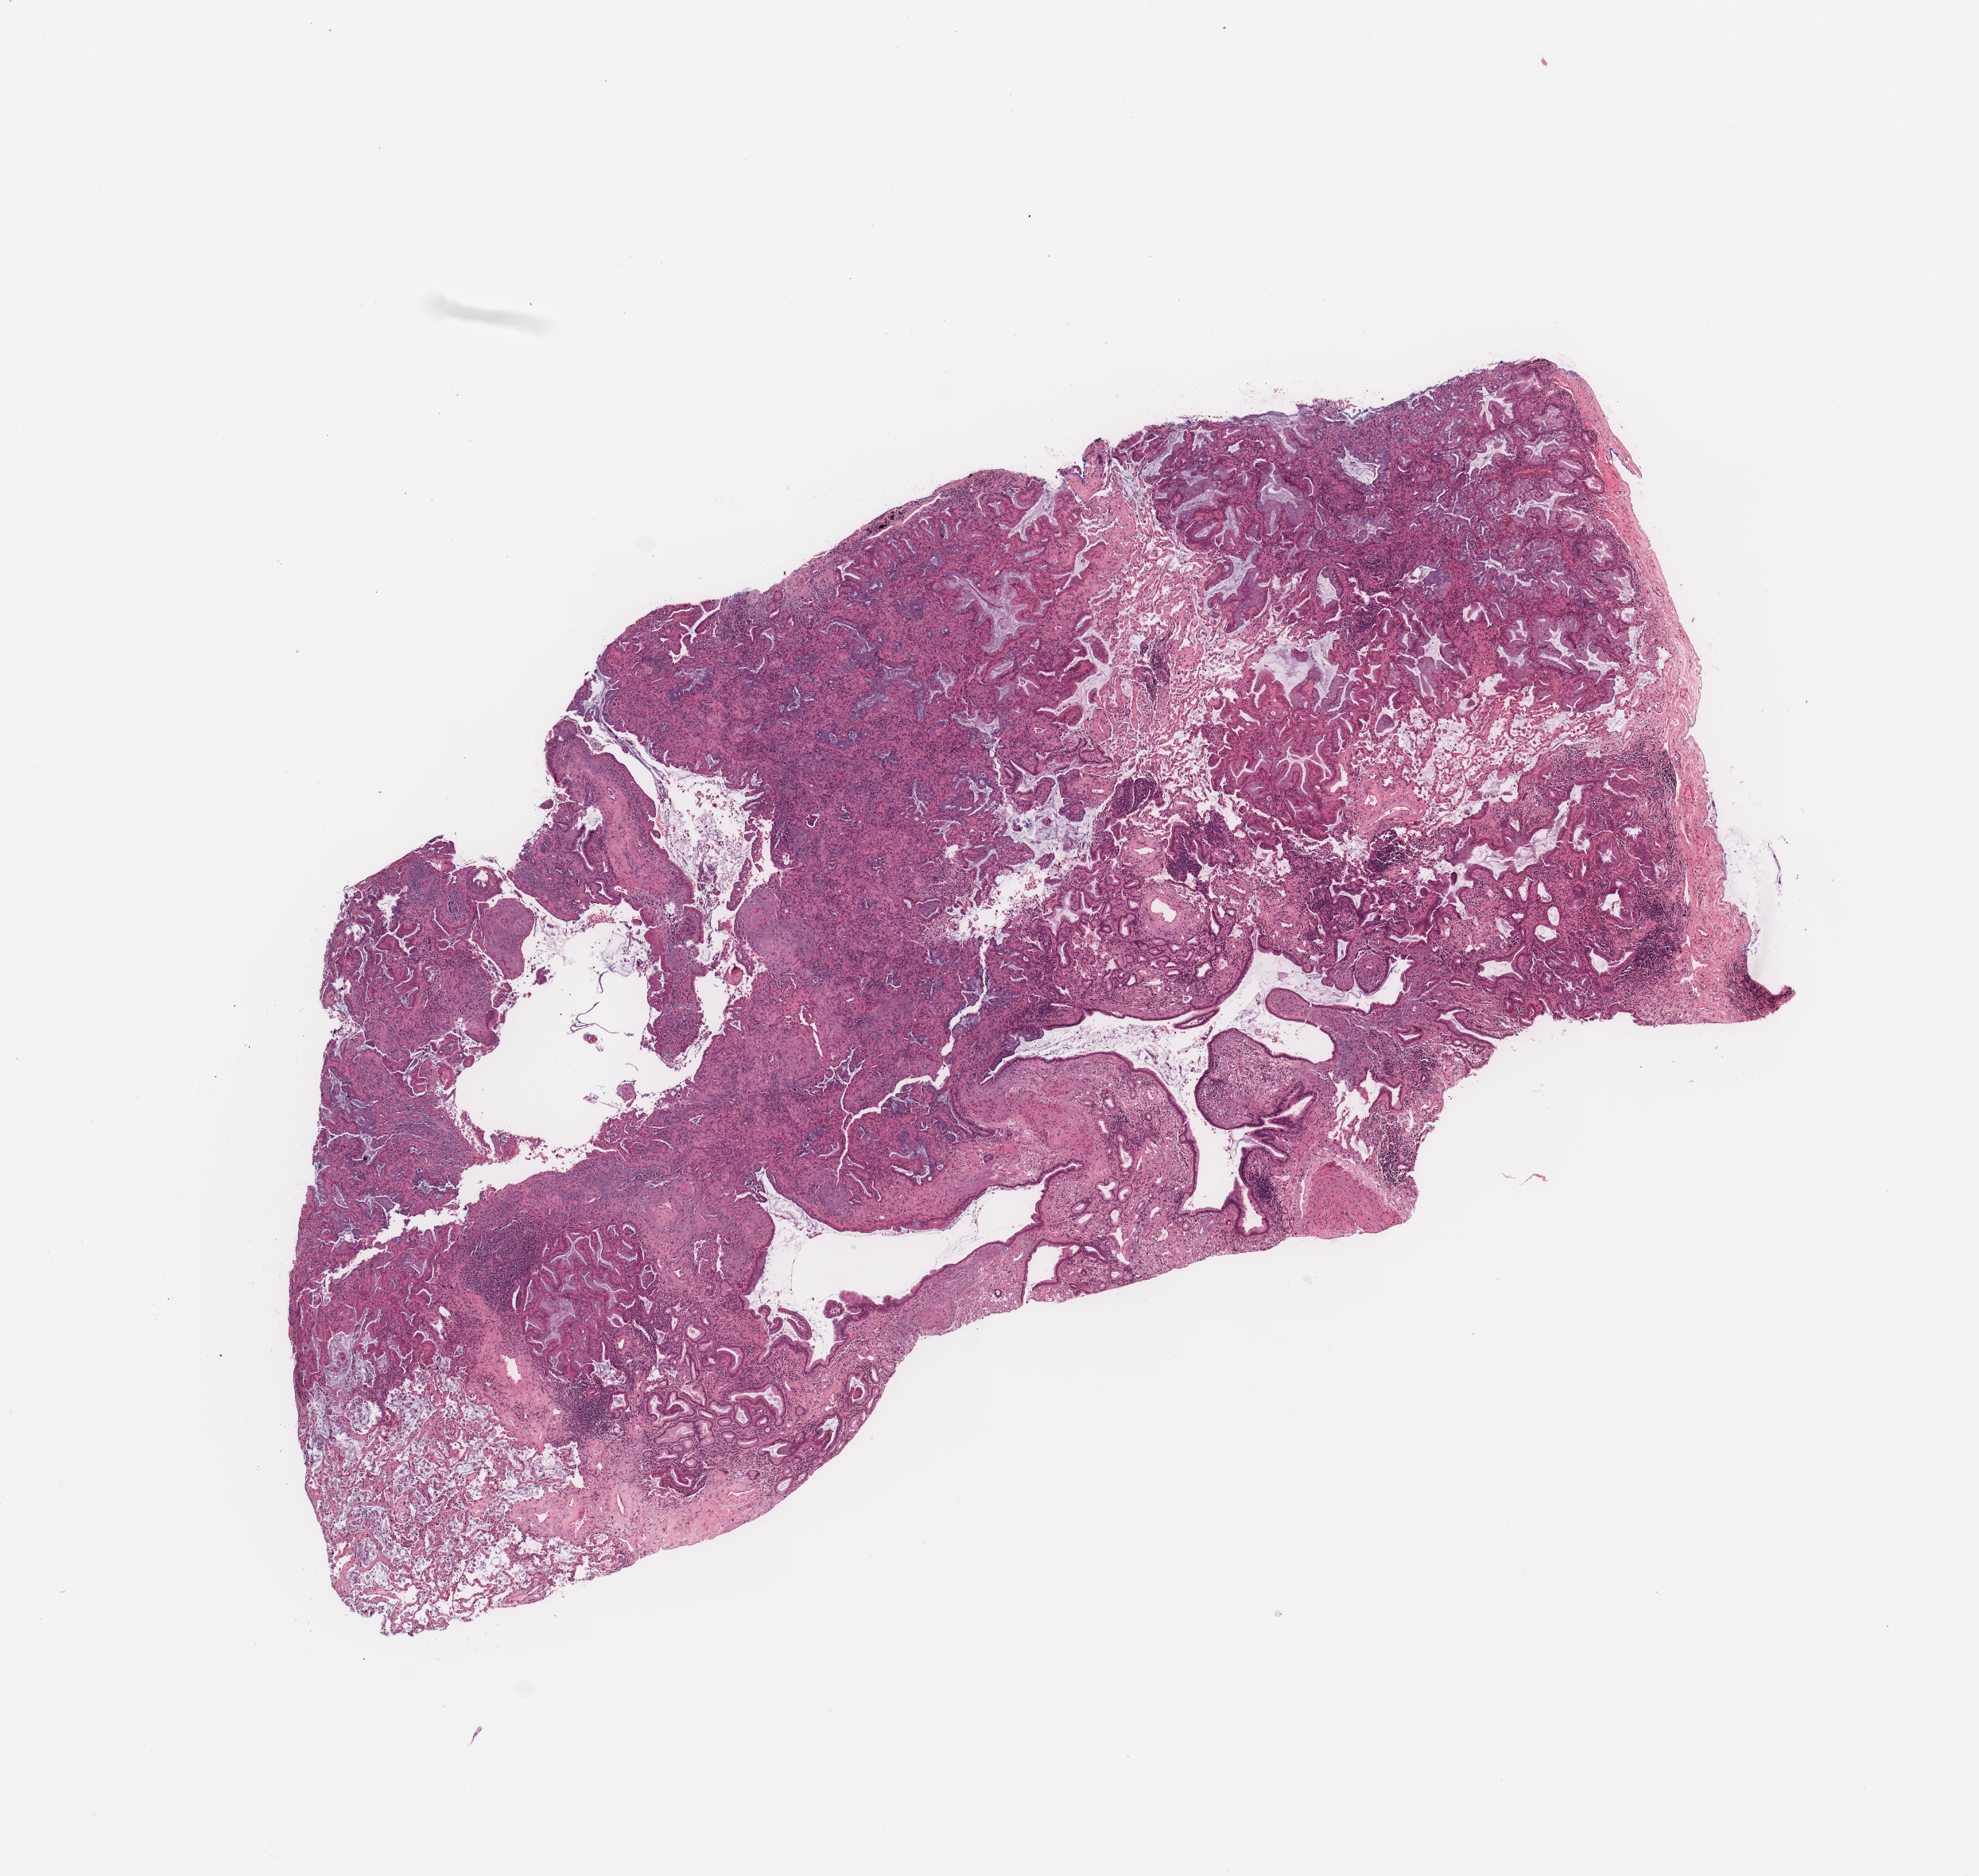
Digitized Hematoxylin and eosin (H&E) stained tissue section (whole slide), whole scanned area (about 9.8 x 9.3 mm, slide scanned at 20x) shown as a low-resolution overview. Tumour tissue sample, sampled site: lung. 78-year-old female patient. Histologic grade: G1 (well differentiated). Pathologist review of this section (percent, as recorded): tumour nuclei 75%, necrosis 5%.
* AJCC pathologic stage: IA
* histologic diagnosis: Adenocarcinoma, NOS